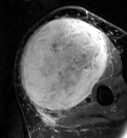
MRI of an extremity soft-tissue mass, one axial slice; slice 38 of 87 in the series (ordered by position); T2-weighted fat-saturated; MR volume resampled by the dataset authors to the PET/CT grid (not the native acquisition matrix); 3.27 mm slice thickness; 127 × 138 image matrix, field of view 124 × 135 mm. Female patient. Case-level facts recorded for this patient, not image findings: histological type: pleiomorphic leiomyosarcoma; grade: high; site of the primary tumour: left biceps.
Outlined on this slice (expert contour drawn on MRI and transferred to this co-registered scan by the dataset authors):
- gross tumour volume including surrounding oedema: bounding box (x1, y1, x2, y2) in pixels: (20, 18, 108, 113)
- gross tumour volume (mass): (20, 18, 108, 113)